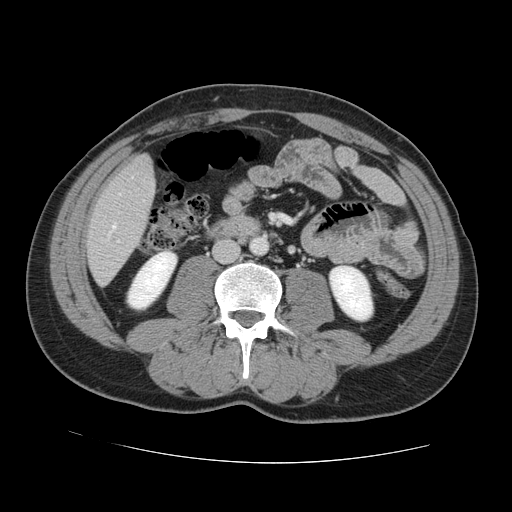
Contrast-enhanced abdominal CT, one axial slice; position 29 of 131 along the scan axis; 120 kVp; intravenous contrast given; soft-tissue window (W 400 / L 40 HU); 2.5 mm slice thickness; 512 × 512 image matrix. Male patient, age 40 years. Case-level facts recorded for this patient, not image findings: diagnosis: colorectal cancer liver metastases, imaged before liver resection.
Annotated regions visible in this slice (expert manual segmentation):
- hepatic veins: box from (x=109, y=194) to (x=120, y=235) px
- liver: (x=88, y=156)–(x=154, y=283)